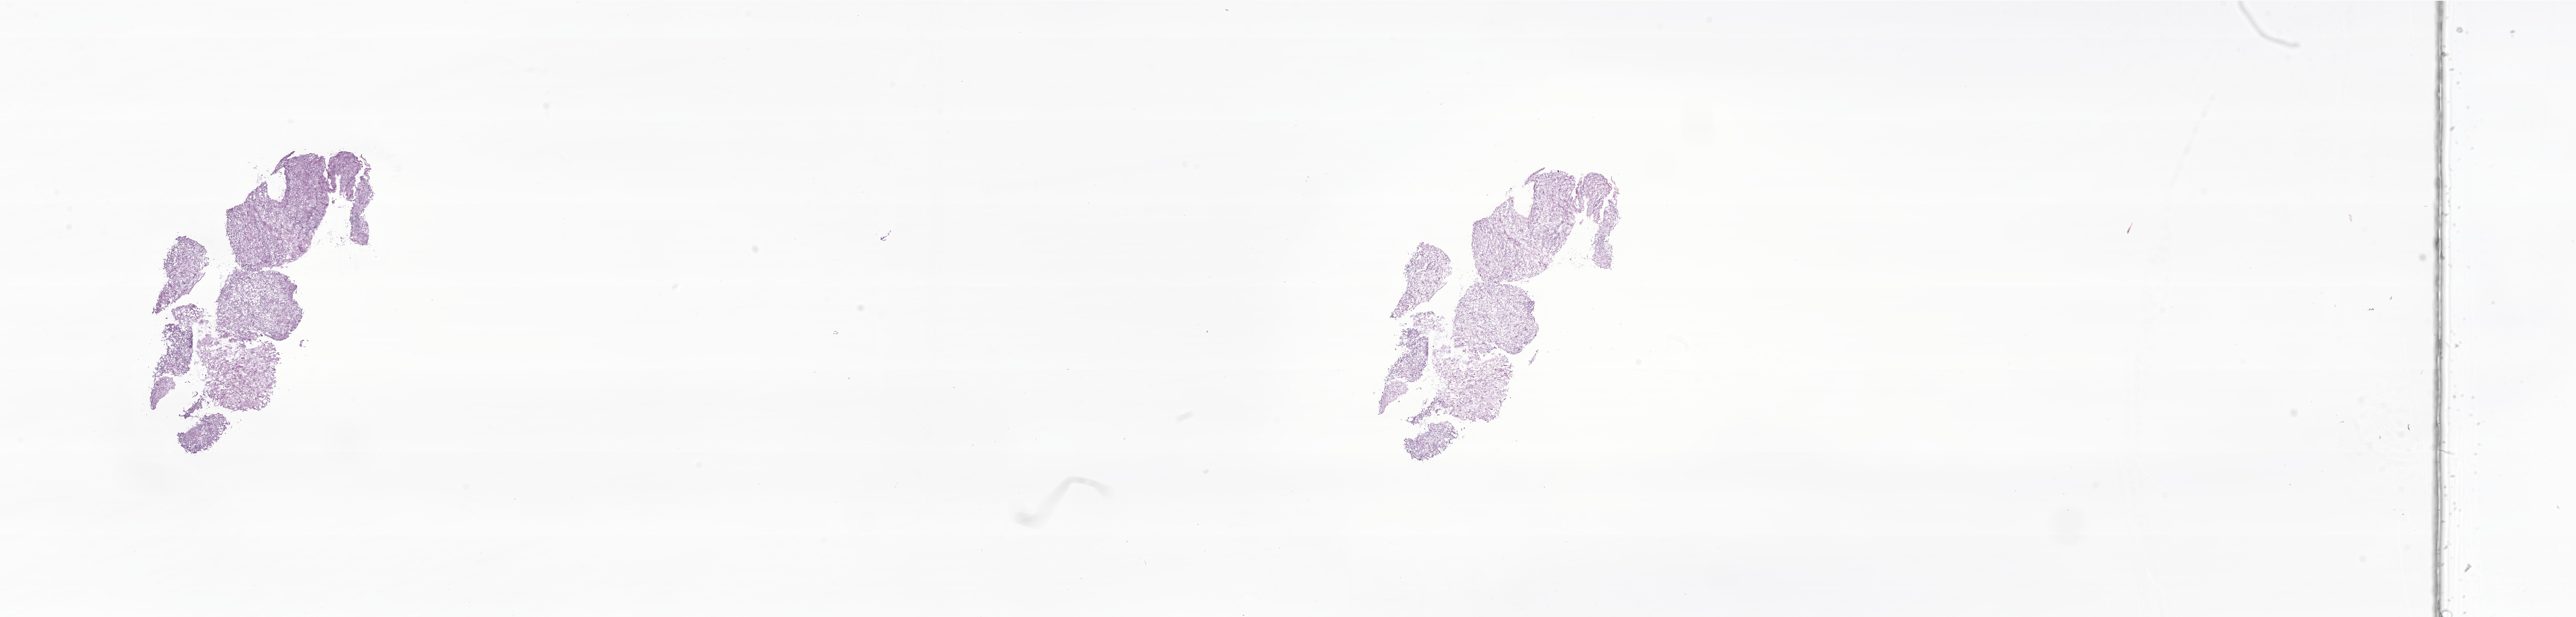
Whole-slide image, haematoxylin and eosin stain of tumor tissue from the pelvis, a low-resolution overview of the entire scanned area, about 33.2 x 7.9 mm, cryosection (OCT / tissue freezing medium). Male patient, age 138 months.
Diagnosis (ICD-O-3 morphology term): Embryonal rhabdomyosarcoma, NOS.